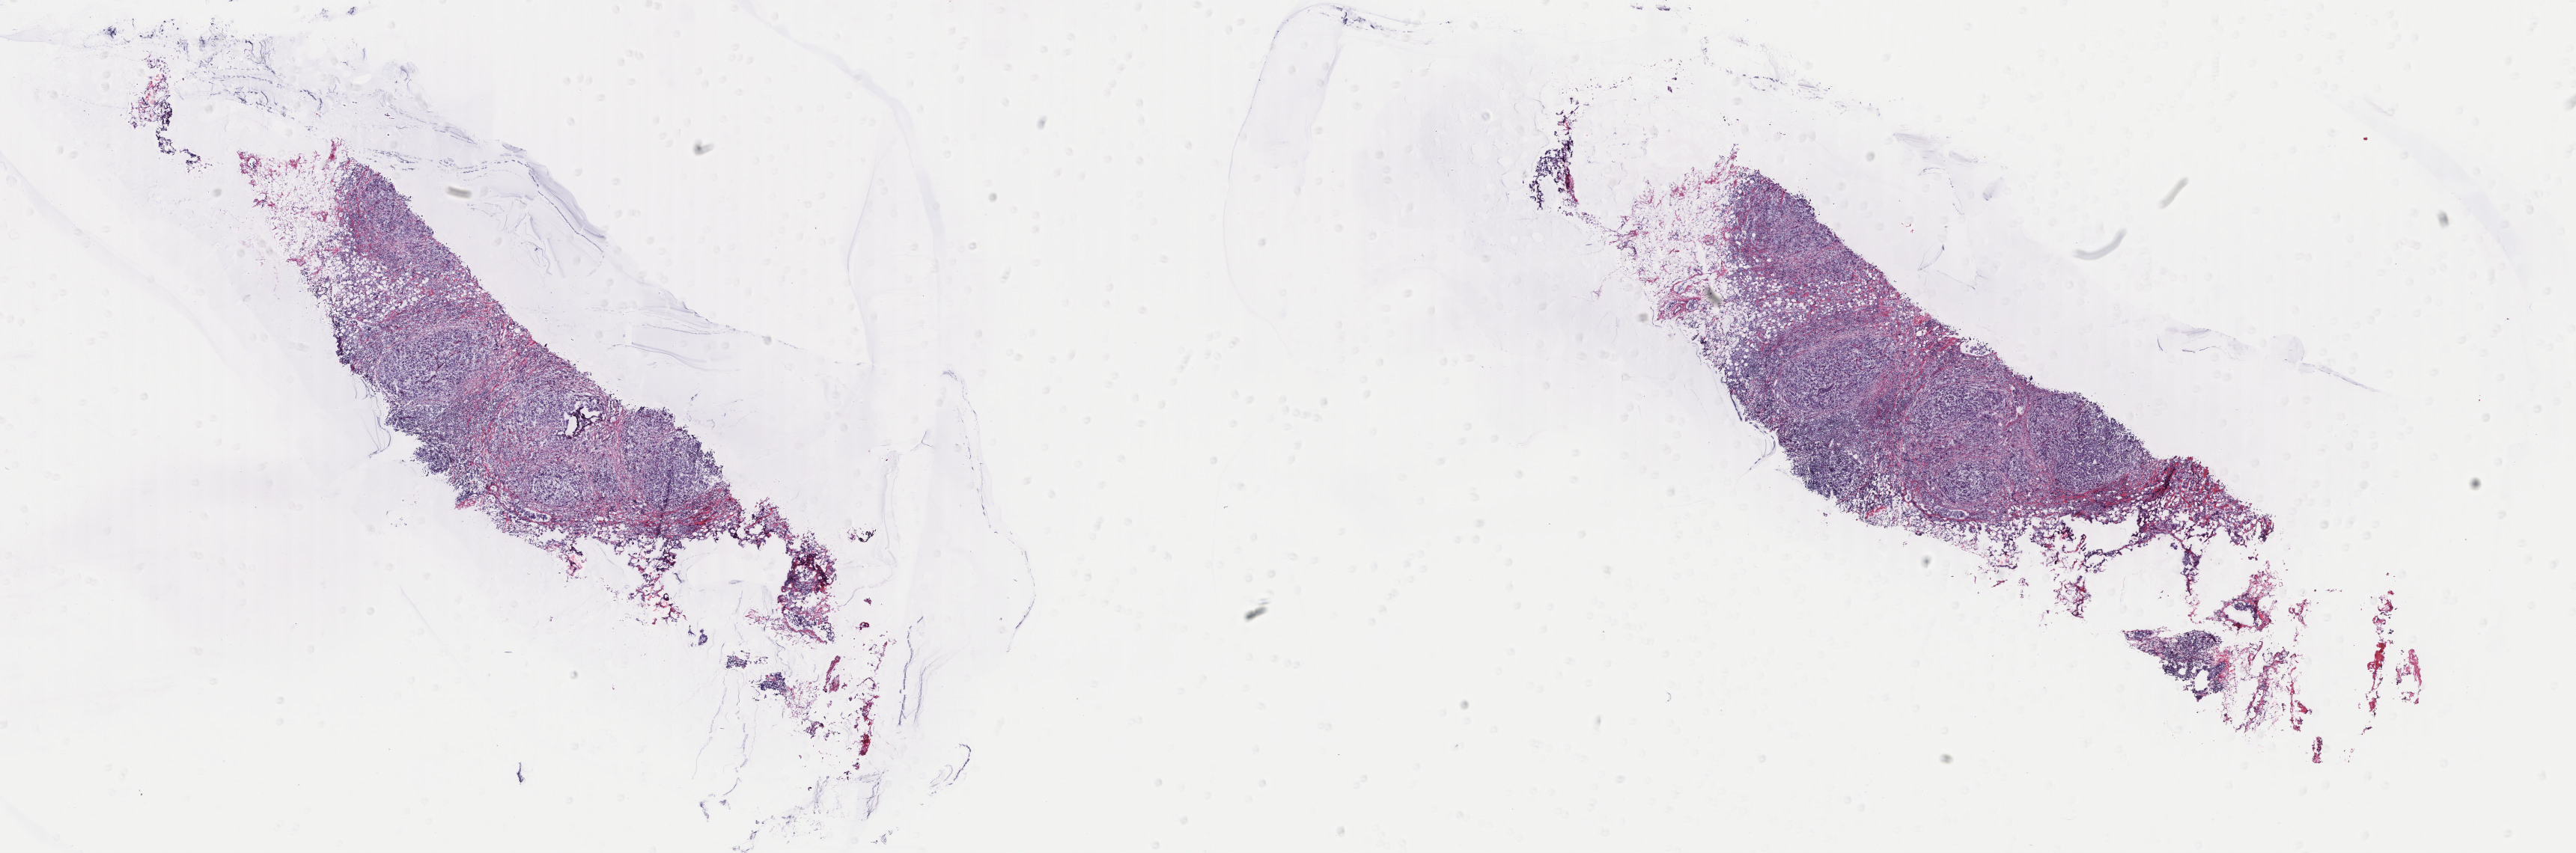
Hematoxylin and eosin (H&E) stained whole-slide image, shown as a low-resolution overview of the whole scanned area (about 27.4 x 9.1 mm, acquisition: 40x scan). Frozen section from the top of the tissue portion. Sample: primary tumour, breast. Female, age 37 years at initial diagnosis. Composition of this section per pathologist review: tumour cells 70%, tumour nuclei 60%, normal cells 10%, stromal cells 17%, necrosis 3%. Infiltration values recorded for this section: lymphocyte infiltration 30%, monocyte infiltration 1%, neutrophil infiltration 0%.
Pathologic diagnosis: Infiltrating duct carcinoma, NOS. Lymph nodes positive (case pathology): 9 of 14 examined. AJCC pathologic stage: IIIA. TNM: T3 N2a M0.